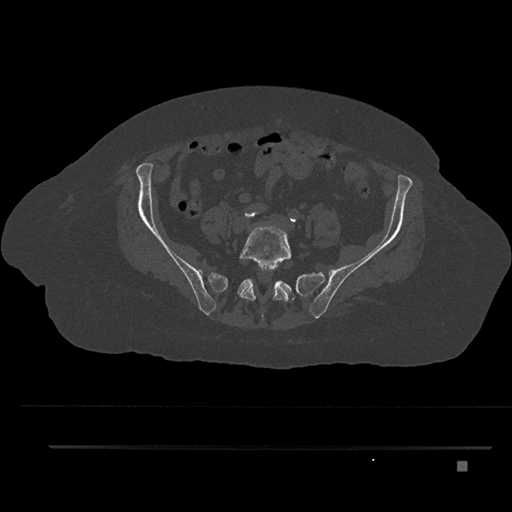
CT including the spine, one axial slice; position 28 of 797 along the scan axis; reconstruction kernel Br40s/3; bone window (W 1800 / L 400 HU); 512 × 512 image matrix, field of view 437 × 437 mm. Patient: female, 76 years. Case-level facts recorded for this patient, not image findings: primary cancer: lung.
Annotated regions visible in this slice (semi-automatically segmented with operator editing):
- L5 vertebra: box from (x=239, y=224) to (x=292, y=320) px